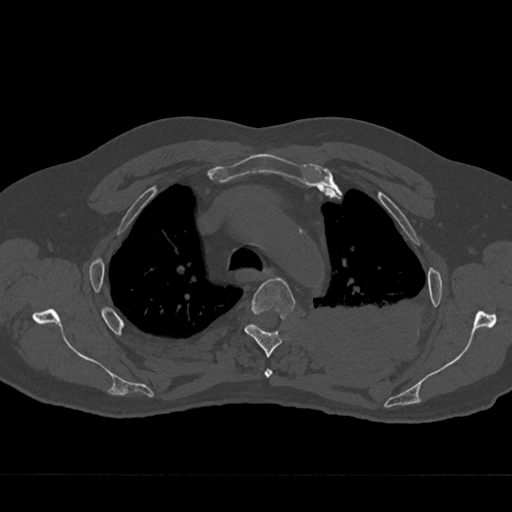
CT including the spine, one axial slice; slice 521 of 797 in the series (ordered by position); 120 kVp; bone window (W 1800 / L 400 HU); 0.5 mm slice thickness; 512 × 512 image matrix, field of view 377 × 377 mm. Male patient, age 75 years. From the clinical record (not read from this slice): primary cancer: renal.
Structures marked on this image (semi-automatically segmented with operator editing):
- T3 vertebra: box from (x=264, y=369) to (x=273, y=378) px
- T4 vertebra: (x=244, y=278)–(x=296, y=357)